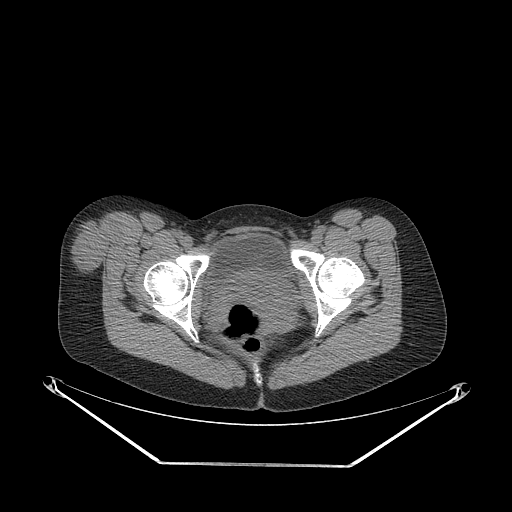
CT of an extremity soft-tissue mass (from a PET/CT study), one axial slice; position 66 of 267 along the scan axis; 140 kVp; soft-tissue window (W 400 / L 40 HU); 3.75 mm slice thickness; 512 × 512 image matrix, field of view 500 × 500 mm. Female patient. Case-level facts recorded for this patient, not image findings: histological type: synovial sarcoma; grade: intermediate; site of the primary tumour: right thigh.
Structures marked on this image (expert contour drawn on MRI and transferred to this co-registered scan by the dataset authors):
- gross tumour volume including surrounding oedema: bounding box [x1, y1, x2, y2] px = [71, 219, 122, 275]
- gross tumour volume (mass): [71, 219, 122, 273]